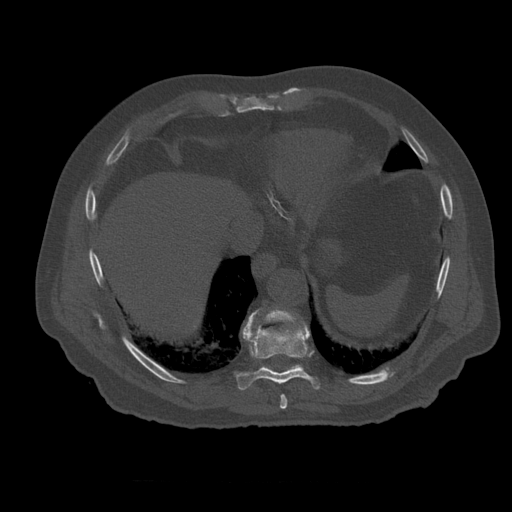
CT including the spine, one axial slice; position 319 of 399 along the scan axis; reconstruction kernel STANDARD; bone window (W 1800 / L 400 HU); 512 × 512 image matrix. Patient age 73 years. Case-level facts recorded for this patient, not image findings: primary cancer: prostate.
Outlined on this slice (semi-automatically segmented with operator editing):
- T10 vertebra: bounding box (x1, y1, x2, y2) in pixels: (265, 310, 304, 369)
- T8 vertebra: (280, 395, 288, 409)
- T9 vertebra: (236, 311, 320, 391)